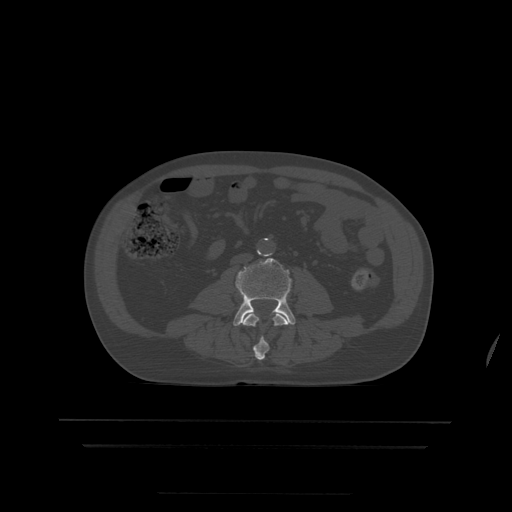
CT including the spine, one axial slice; slice 105 of 522 in the series (ordered by position); bone window (W 1800 / L 400 HU); 1.25 mm slice thickness; 512 × 512 image matrix, field of view 436 × 436 mm. Patient age 68 years. From the clinical record (not read from this slice): primary cancer: urothelial.
Structures marked on this image (semi-automatically segmented with operator editing):
- L3 vertebra: box from (x=242, y=313) to (x=292, y=360) px
- L4 vertebra: (x=233, y=258)–(x=296, y=327)